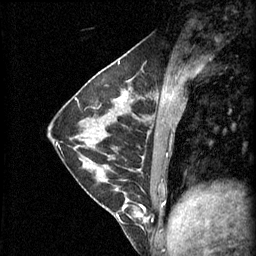
Breast MRI (dynamic contrast-enhanced), one sagittal slice. Position 21 of 60 along the scan axis. 3 images stored at this slice position (order not interpretable as contrast timing). 1.5 T. TE 4.2 ms, TR 11 ms. 2.1 mm slice thickness. 256 × 256 image matrix, field of view 180 × 180 mm. Patient: female, 29 years.
Outlined on this slice (semi-automatically segmented with operator editing):
- analysis volume of interest (the breast-tissue region the enhancement analysis was run in; not a lesion): bounding box (x1, y1, x2, y2) in pixels: (93, 164, 153, 223)
- tumour enhancement mask (voxels above the 70 % enhancement threshold inside the analysis volume of interest): (117, 170, 148, 221)